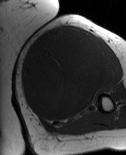
MRI of an extremity soft-tissue mass, one axial slice. MR volume resampled by the dataset authors to the PET/CT grid (not the native acquisition matrix). 3.27 mm slice thickness. 126 × 155 image matrix, field of view 123 × 151 mm. Female patient. From the clinical record (not read from this slice): histological type: pleiomorphic leiomyosarcoma; grade: high; site of the primary tumour: left biceps.
Structures marked on this image (expert contour drawn on MRI and transferred to this co-registered scan by the dataset authors):
- gross tumour volume including surrounding oedema: bounding box [x1, y1, x2, y2] px = [20, 26, 110, 121]
- gross tumour volume (mass): [20, 28, 110, 121]